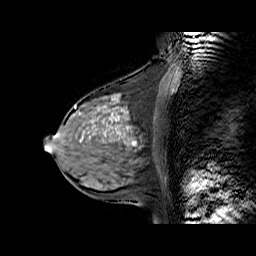
Breast MRI (dynamic contrast-enhanced), one sagittal slice; position 27 of 60 along the scan axis; dynamic contrast-enhanced series, time point 2 of 6 at this slice position (early post-contrast); 1.5 T; TE 6.3 ms, TR 32.9 ms; 4 mm slice thickness; 256 × 256 image matrix, field of view 200 × 200 mm. Female patient. From the clinical record (not read from this slice): setting: breast cancer imaged before/during neoadjuvant chemotherapy; receptor status: HR-positive, HER2-negative.
Outlined on this slice (semi-automatically segmented with operator editing):
- analysis volume of interest (the breast-tissue region the enhancement analysis was run in; not a lesion): bounding box <57,86,169,170> (left, top, right, bottom; pixels)
- tumour enhancement mask (voxels above the 100 % enhancement threshold inside the analysis volume of interest): <82,98,136,145>